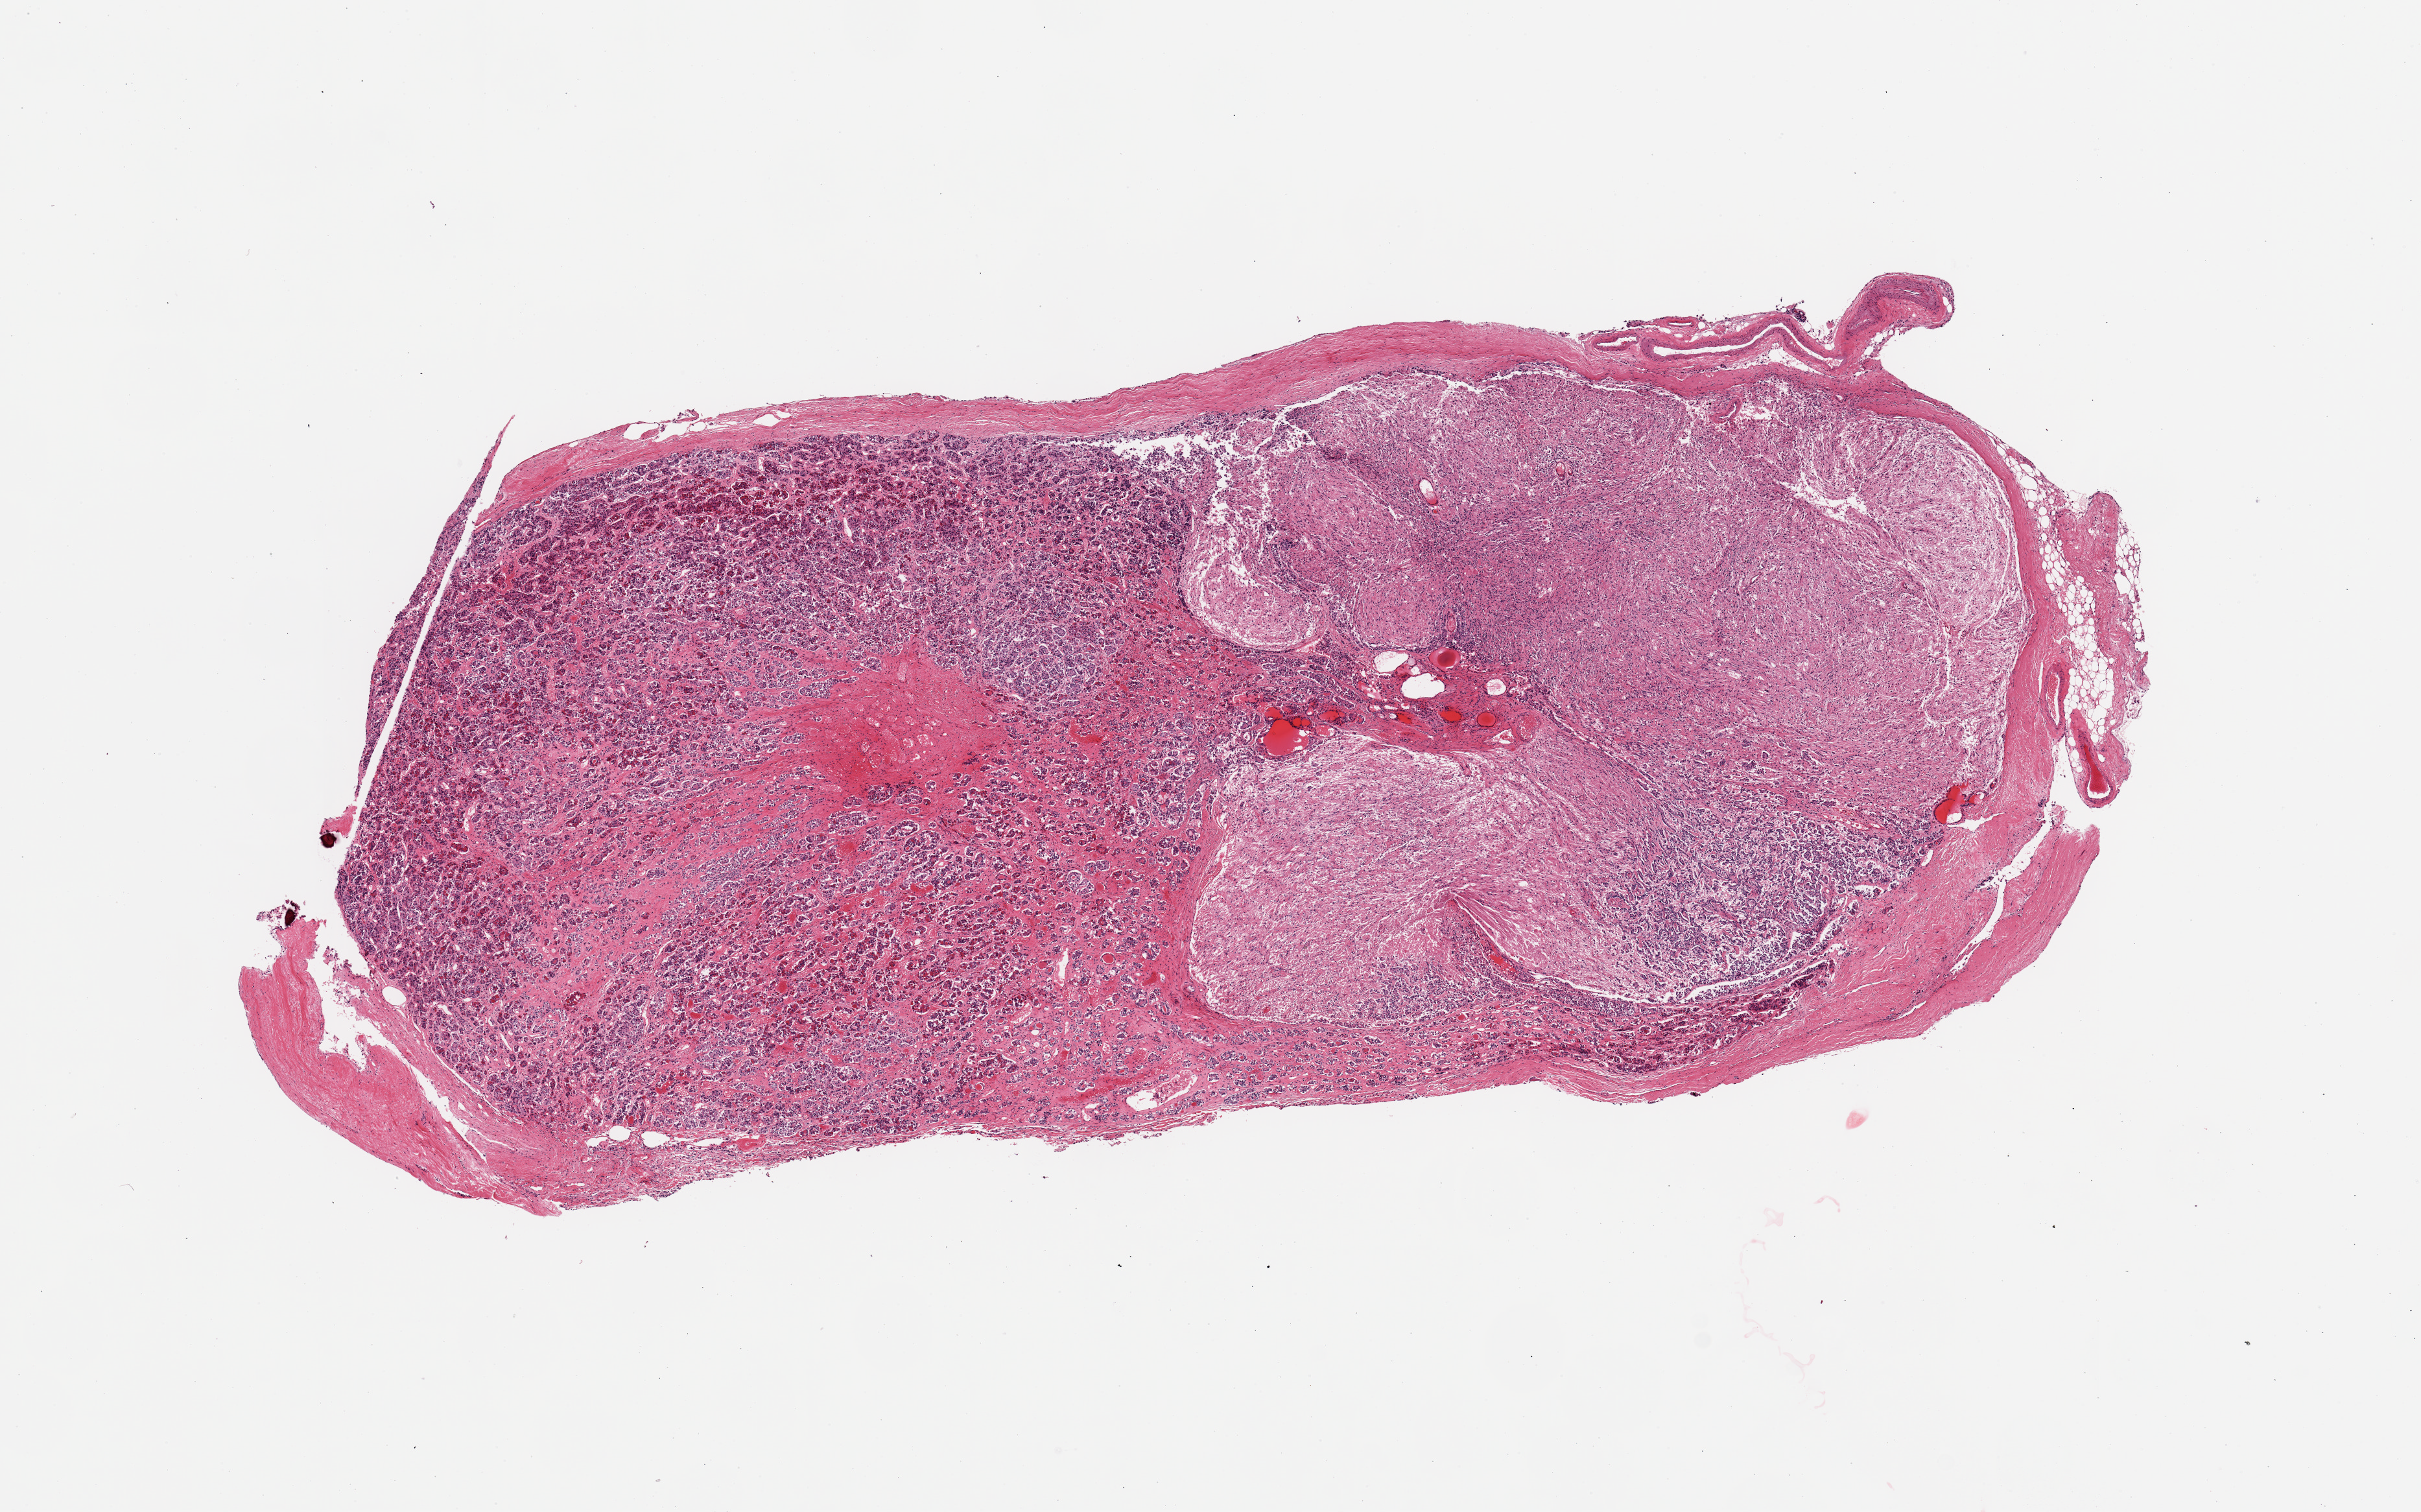
Digitized H&E-stained section, brightfield — whole scanned area (about 14.8 x 9.2 mm) shown as a low-resolution overview, PAXgene-fixed, paraffin-embedded tissue, sampled site (target tissue): pituitary, donor tissue sample. Donor: male.
Review note (as recorded): 1 pieces; adenohypophysis and neurohypophysis.